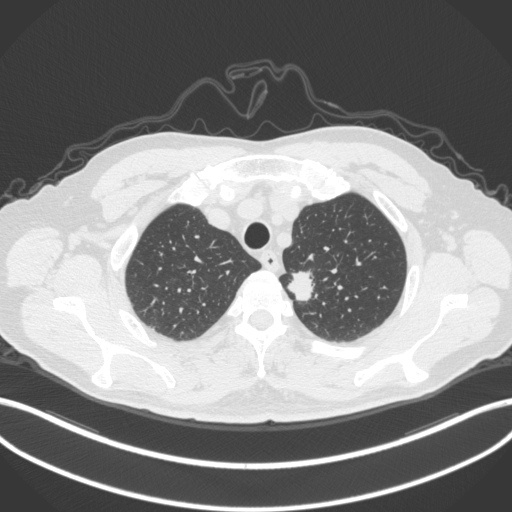
Chest CT, one axial slice. Slice 317 of 382 in the series (ordered by position). Reconstruction kernel B31f. Lung window (W 1500 / L -600 HU). 1 mm slice thickness. 512 × 512 image matrix, field of view 400 × 400 mm. Male patient, age 64 years. Case-level facts recorded for this patient, not image findings: clinical TNM (as recorded): T1c N0 M0.
Outlined on this slice (rectangle marked by the reading radiologist):
- lung tumour (recorded histology: adenocarcinoma): bounding box <283,265,320,309> (left, top, right, bottom; pixels)